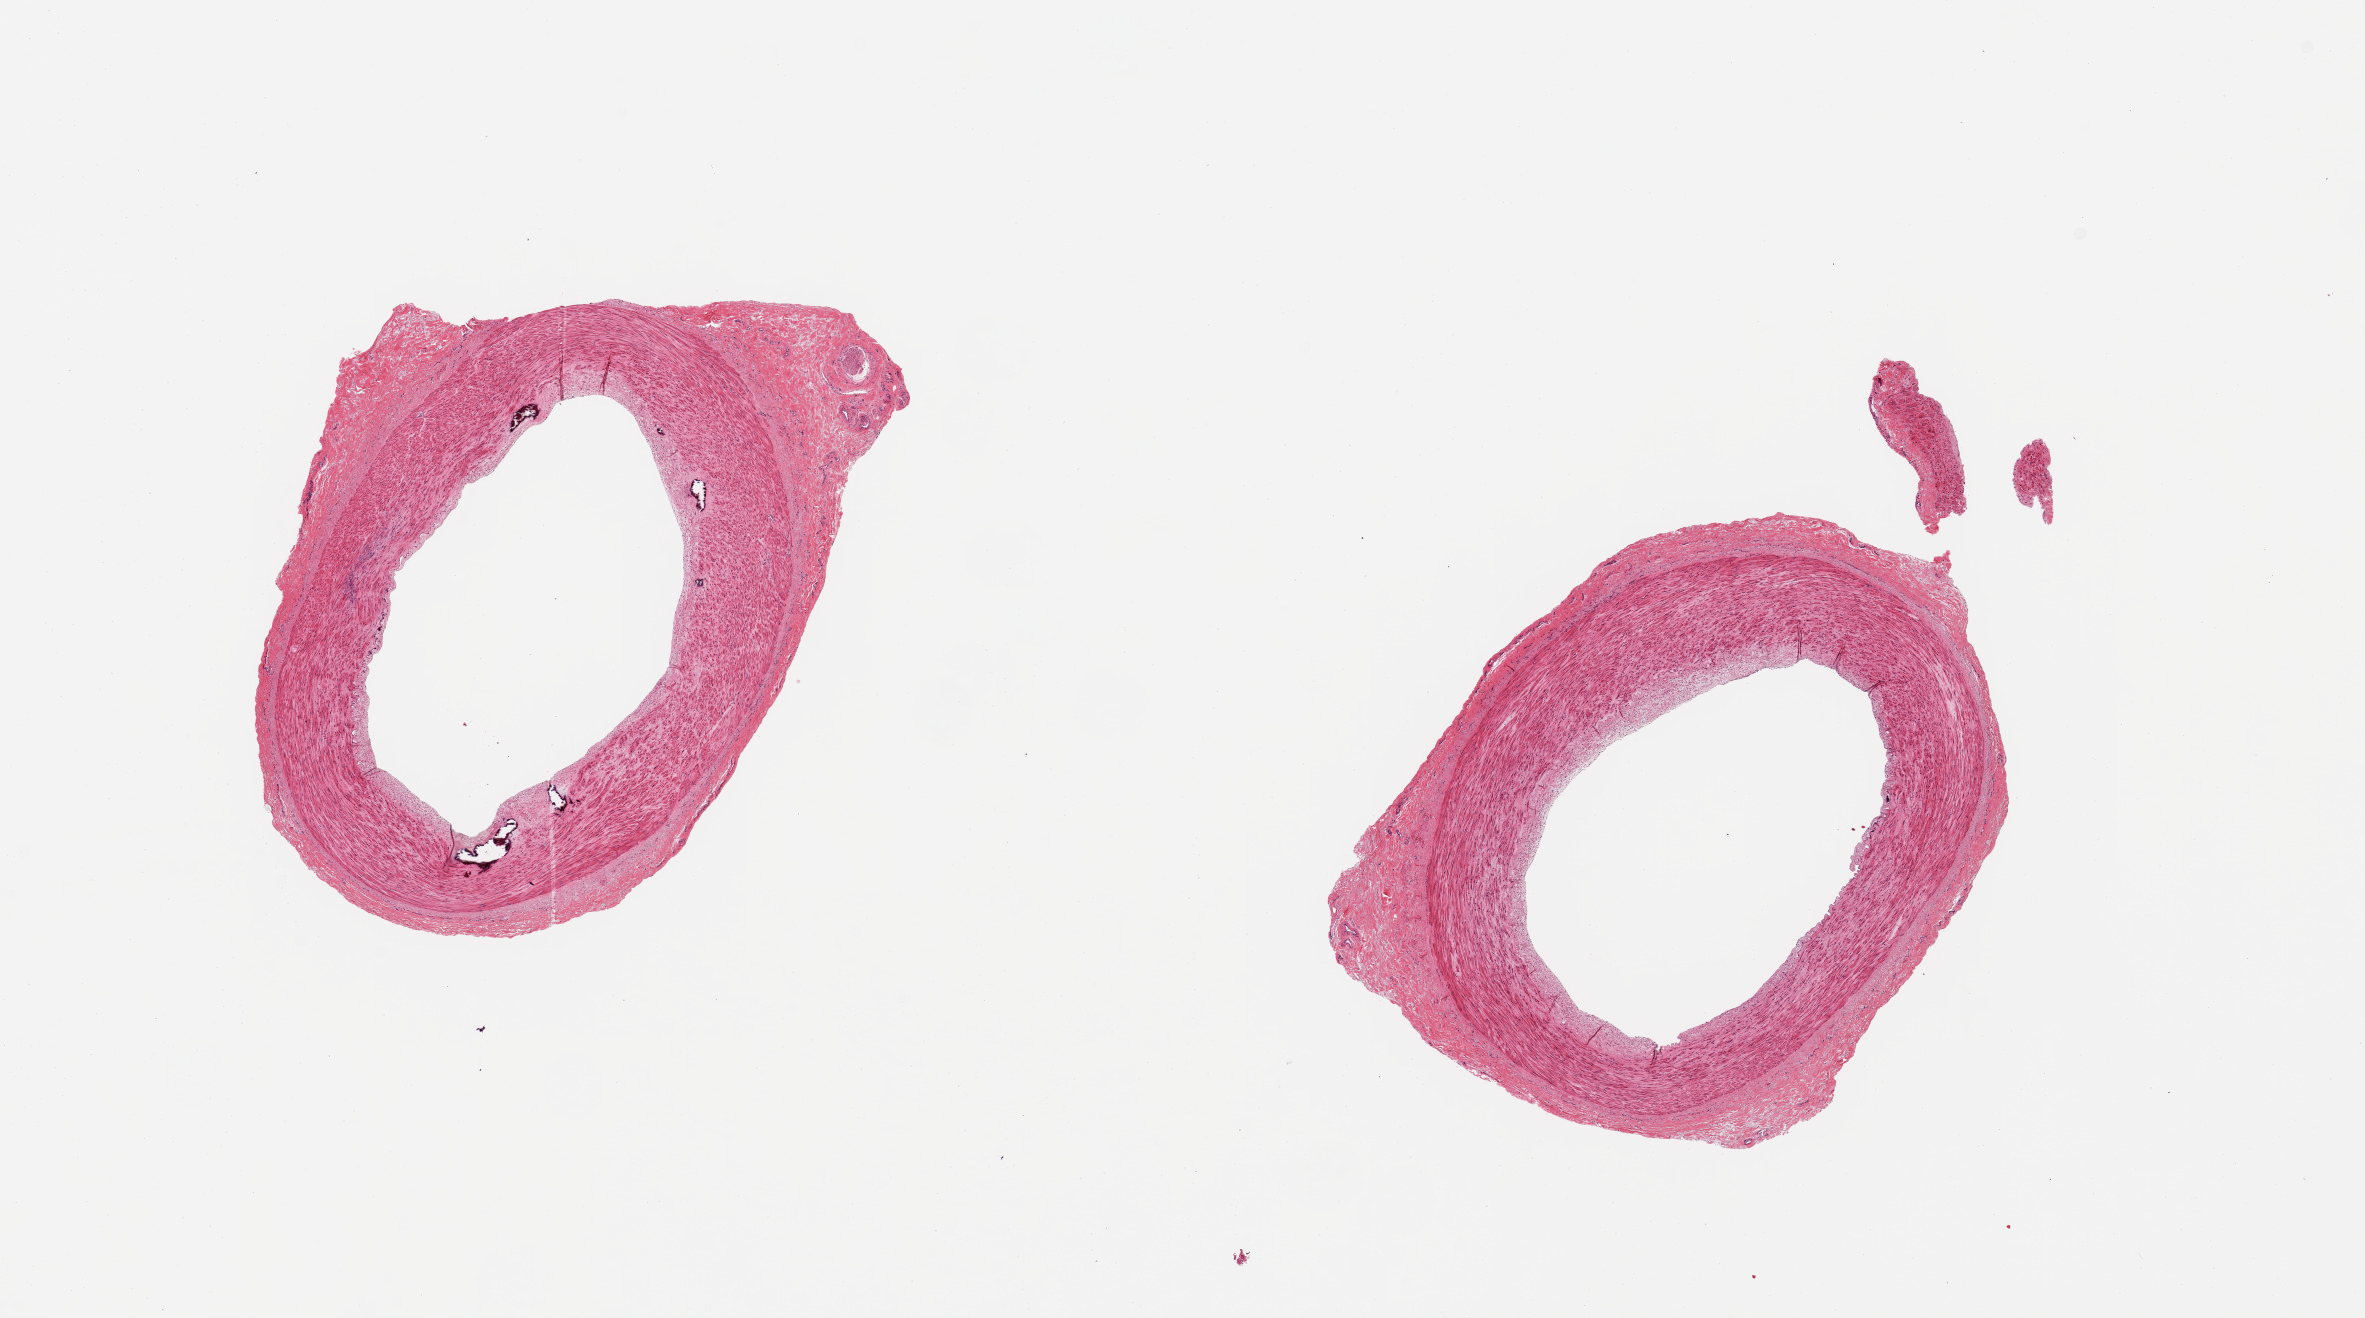
Whole-slide image, haematoxylin and eosin stain, a low-resolution overview of the entire scanned area, about 18.7 x 10.4 mm, PAXgene-fixed paraffin-embedded (PFPE) section, sampled site (target tissue): tibial artery, tissue donor sample. Donor: male.
Review note (as recorded): 2 pieces, clean specimens; focal Monckeberg medial sclerosis (calcifications), excellent specimens.